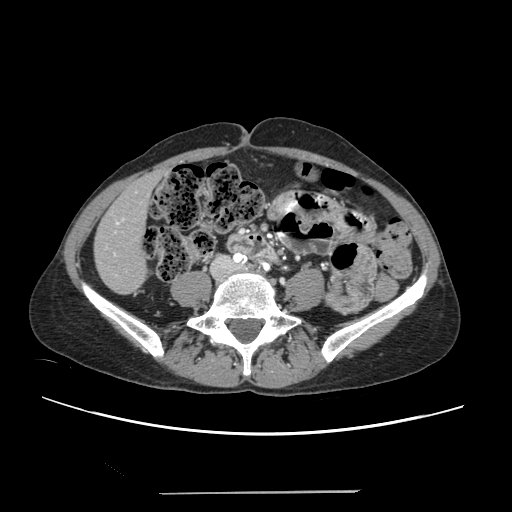
Contrast-enhanced abdominal CT, one axial slice; slice 38 of 240 in the series (ordered by position); 120 kVp; intravenous contrast given; soft-tissue window (W 400 / L 40 HU); 1.25 mm slice thickness; 512 × 512 image matrix. Female patient, age 60 years. Case-level facts recorded for this patient, not image findings: diagnosis: colorectal cancer liver metastases, imaged before liver resection; multiple liver metastases: no; largest metastasis: 1.5 cm.
Annotated regions visible in this slice (expert manual segmentation):
- liver: bounding box <95,174,159,293> (left, top, right, bottom; pixels)
- planned liver remnant (the part of the liver to remain after resection): <95,174,160,293>
- portal vein (with intrahepatic branches): <106,218,124,275>